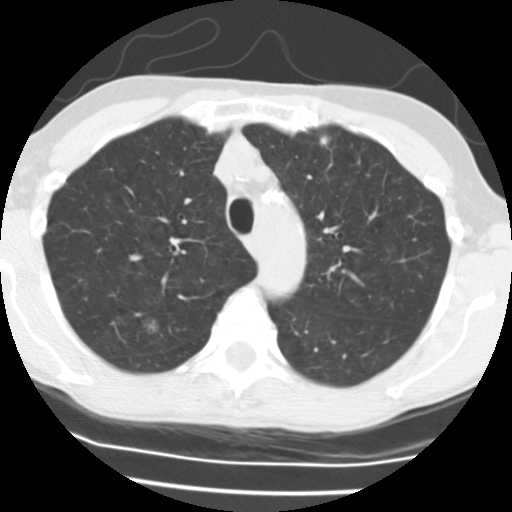
Axial slice from a low-dose chest CT screening exam. Third screening round (two years after baseline). Lung window (W 1500 / L -600 HU). Standard (soft-tissue) reconstruction kernel (STANDARD). Slice 162 of 195 in the series. Female participant, aged 58 years at enrolment. Current smoker at enrolment.
• Expert reader's lesion annotation, bounding box [x1, y1, x2, y2] px = [132, 311, 167, 345].
• The screening reader recorded 3 non-calcified nodules or masses ≥4 mm on this exam (right upper lobe, left upper lobe, right upper lobe); which of them this box marks is not recorded.
• Participant outcome: lung cancer diagnosed 153 days after this screen — bronchiolo-alveolar adenocarcinoma, NOS, right upper lobe, well differentiated (G1), stage IA (AJCC 6th edition), 8 mm at pathology.